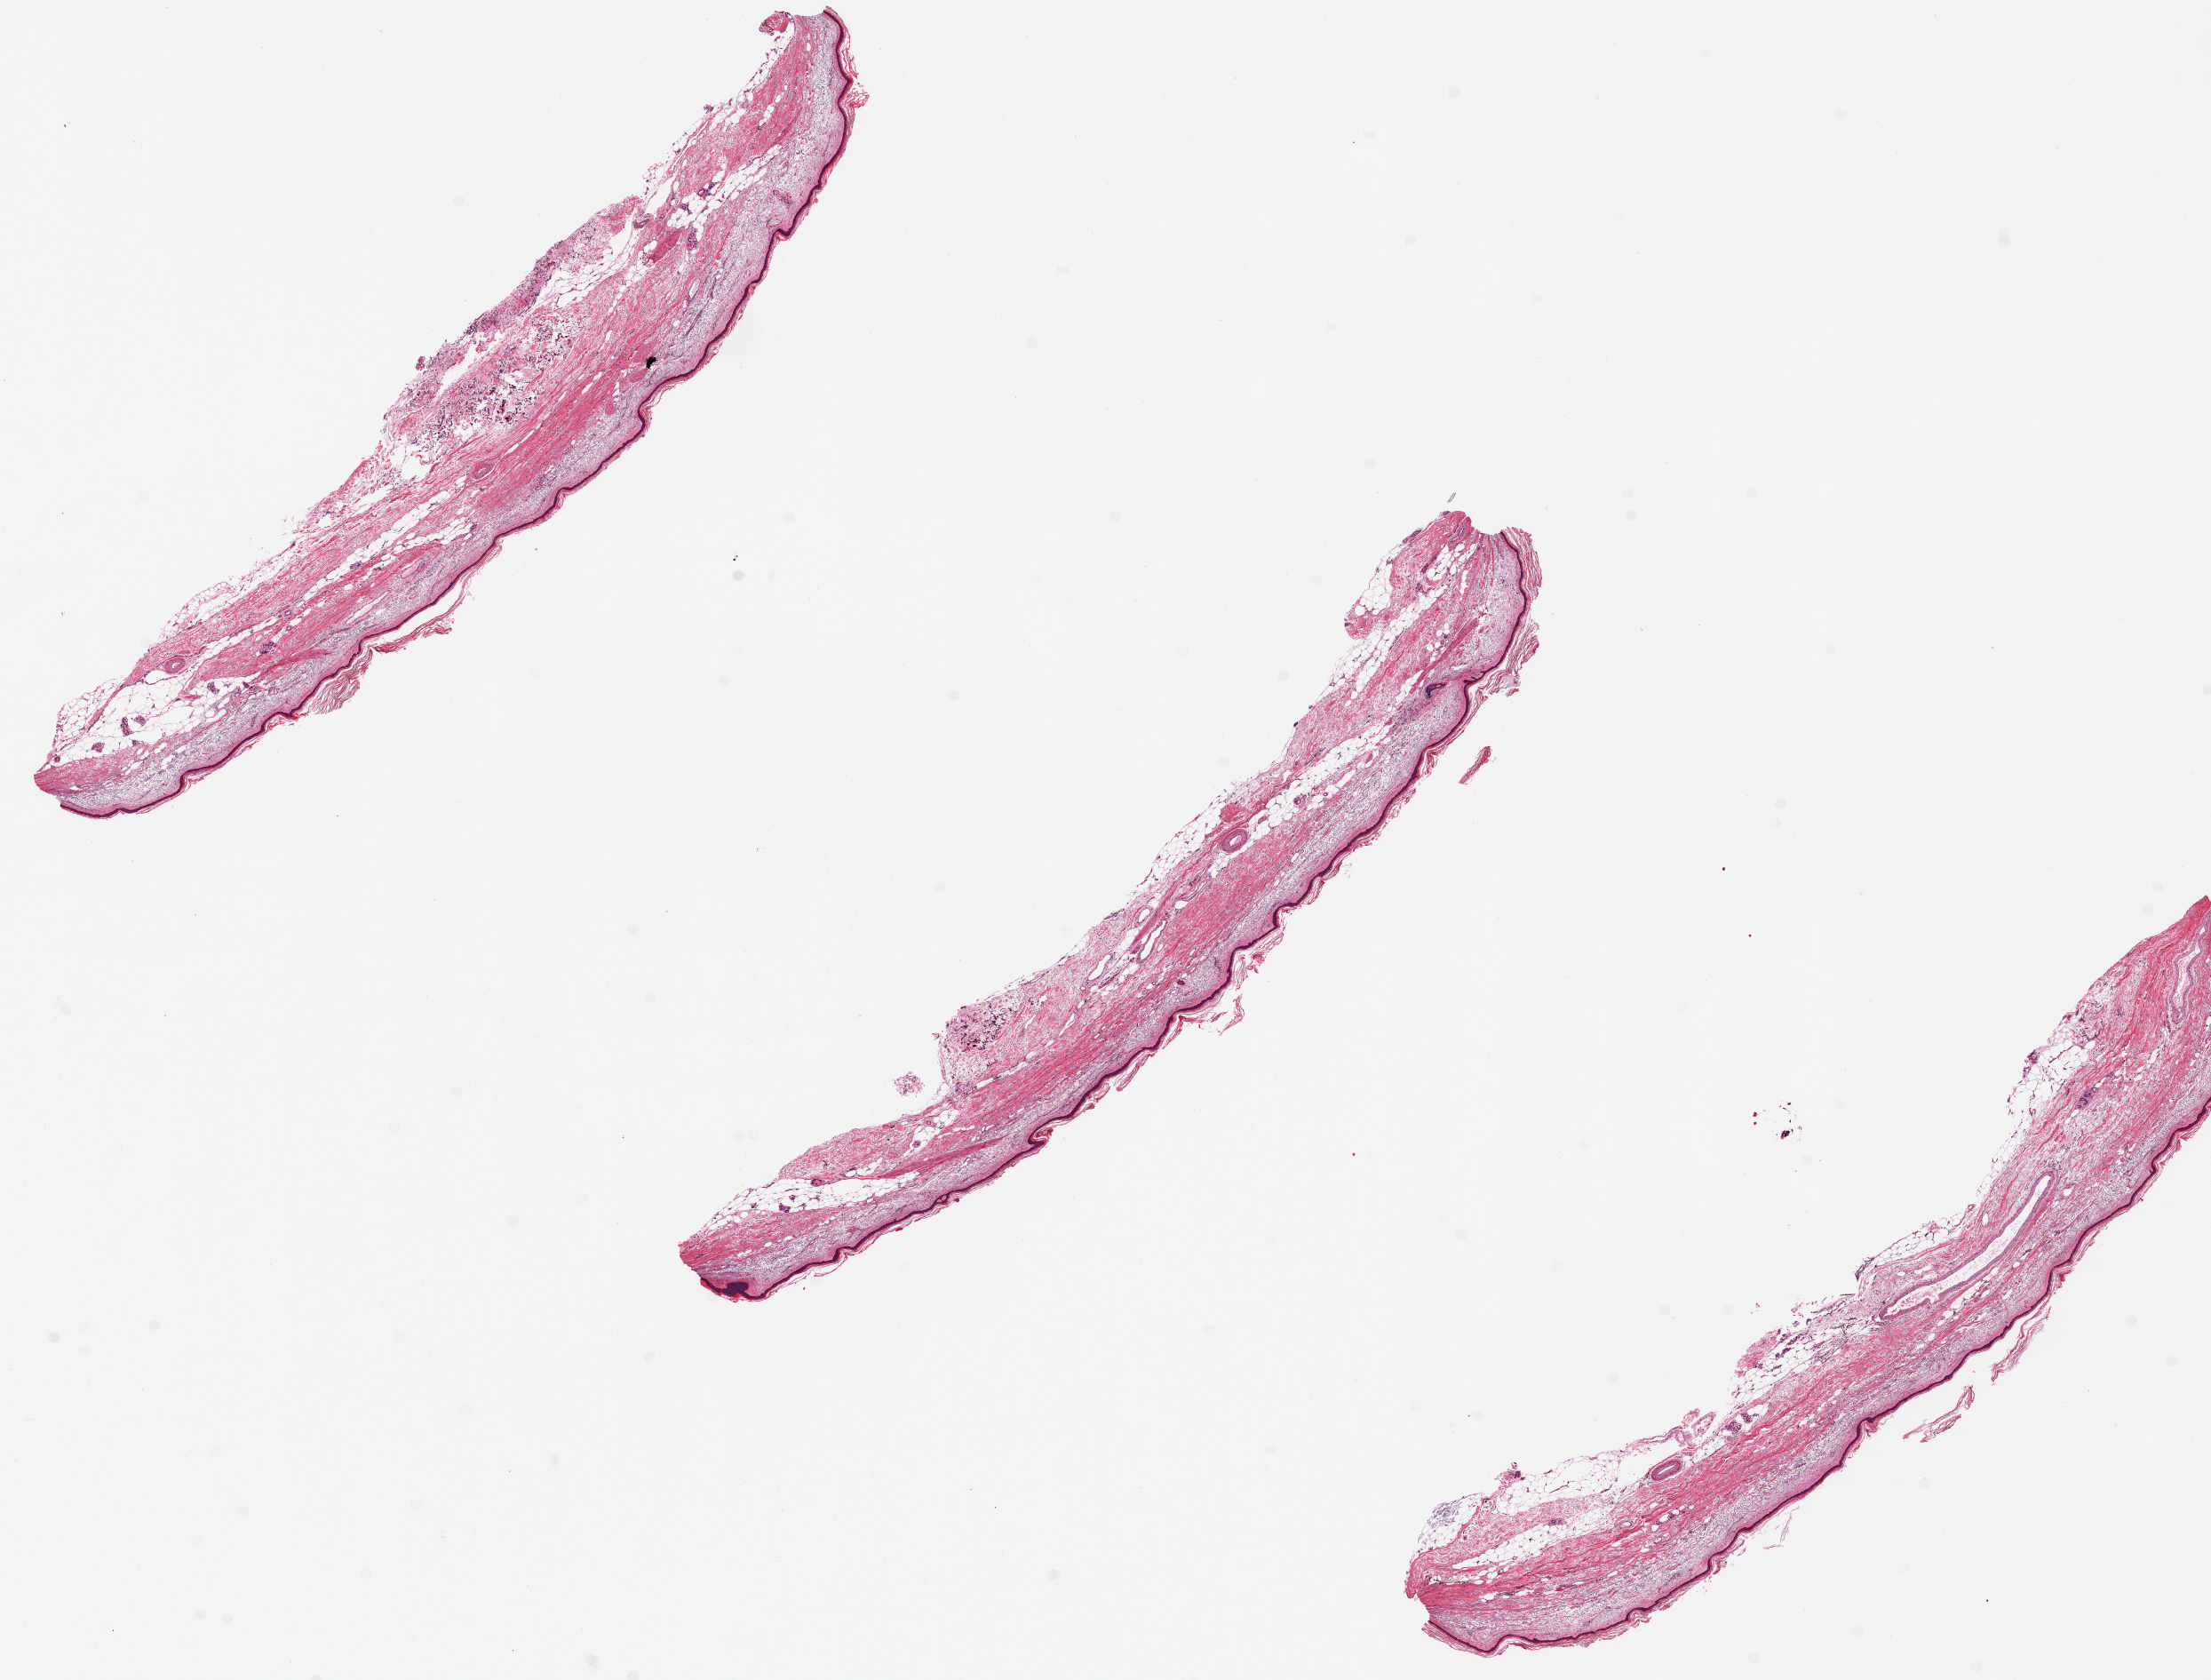
Whole-slide image, hematoxylin and eosin (H&E) stain, brightfield — whole scanned area (about 19.7 x 15.0 mm) shown as a low-resolution overview; PAXgene-fixed, paraffin-embedded tissue; target tissue: skin of lower leg; donor tissue sample. Female donor.
* reviewer comment on this tissue sample: Epidermis is ~2% thickness of specimen. Marked dermal elastosis